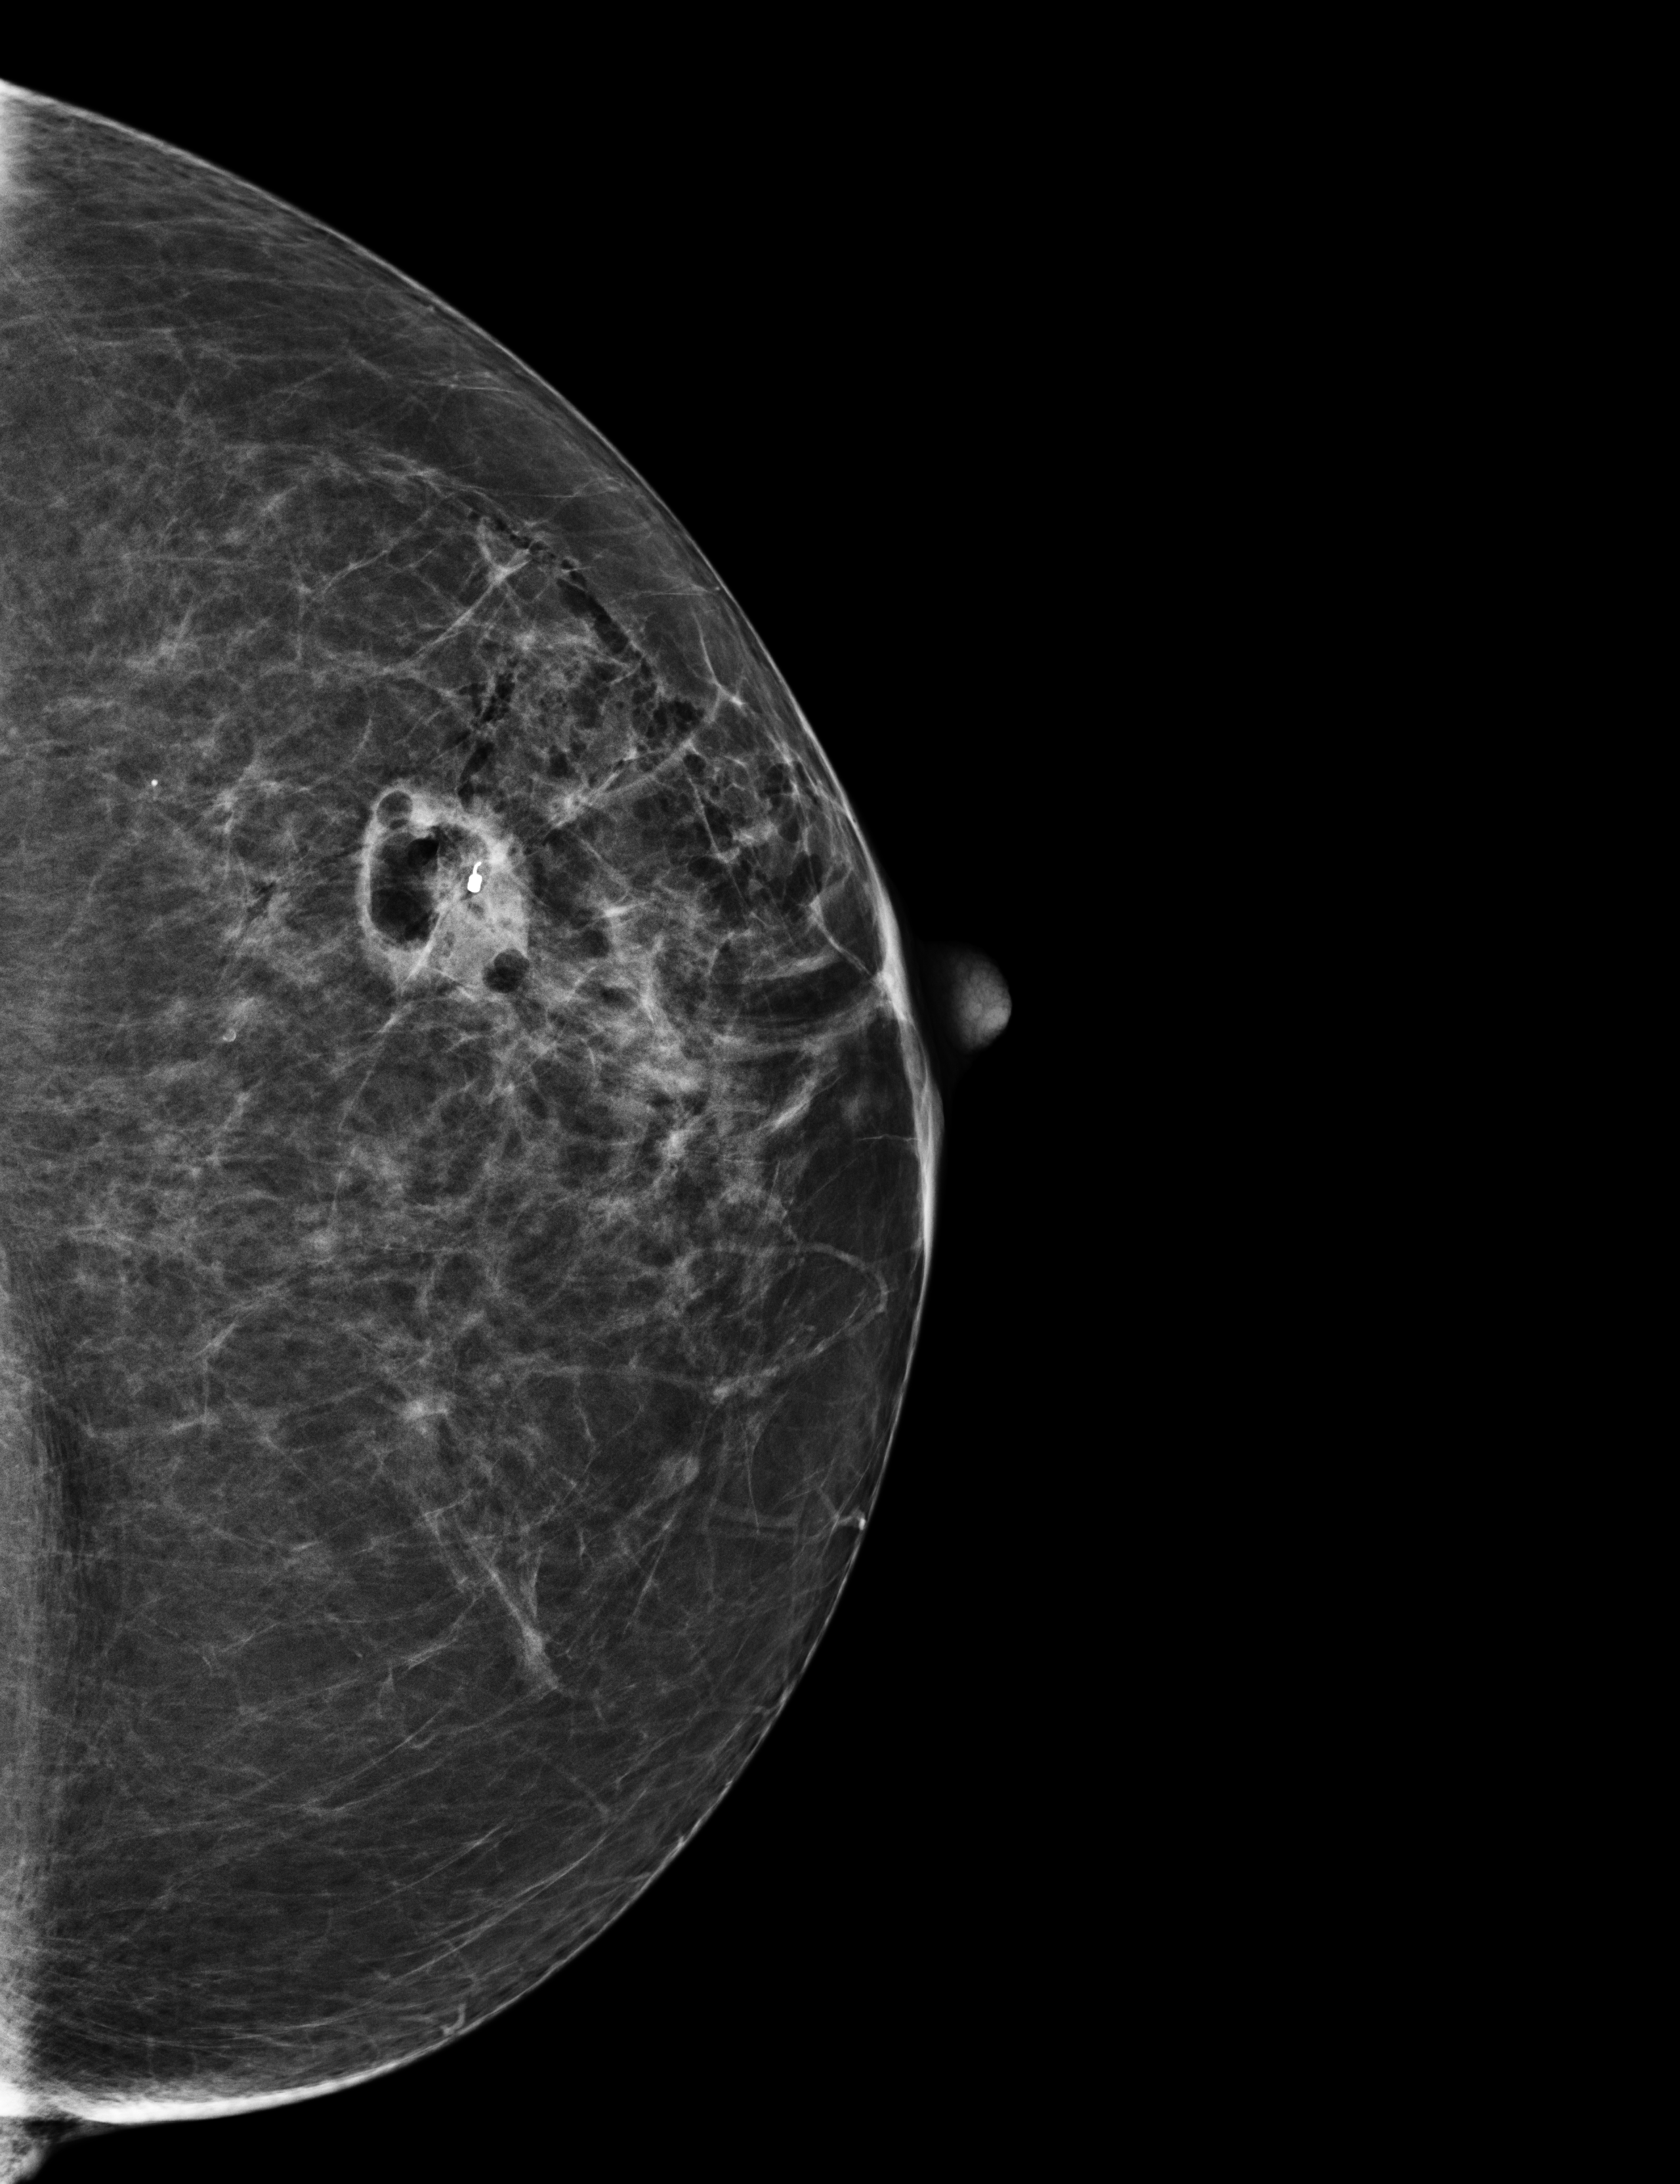
Diagnostic examination (additional views). Patient aged 74 years (female).
Image type: full-field digital mammogram. Breast: left. Projection: craniocaudal (CC) view.